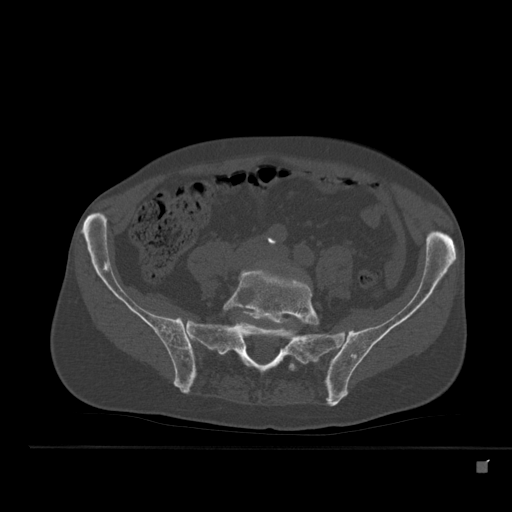
CT including the spine, one axial slice. Slice 119 of 517 in the series (ordered by position). Reconstruction kernel Br40s. 120 kVp. Bone window (W 1800 / L 400 HU). 1.5 mm slice thickness. 512 × 512 image matrix. Male patient, age 70 years. From the clinical record (not read from this slice): primary cancer: renal.
Outlined on this slice (semi-automatically segmented with operator editing):
- L5 vertebra: bounding box [x1, y1, x2, y2] px = [222, 270, 320, 371]